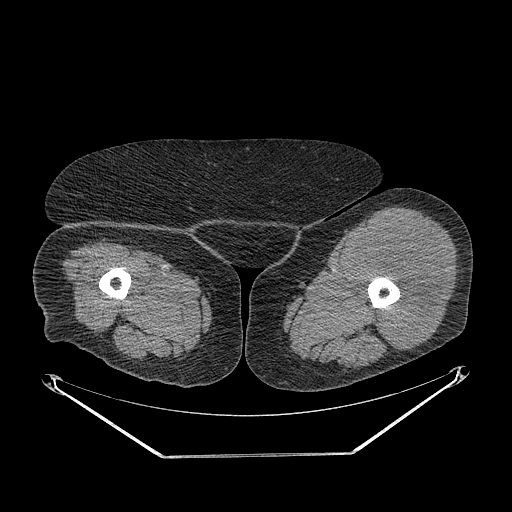
CT of an extremity soft-tissue mass (from a PET/CT study), one axial slice; position 238 of 267 along the scan axis; 140 kVp; soft-tissue window (W 400 / L 40 HU); 512 × 512 image matrix, field of view 500 × 500 mm. Female patient. From the clinical record (not read from this slice): histological type: undifferentiated – high grade; grade: high; site of the primary tumour: left thigh.
Outlined on this slice (expert contour drawn on MRI and transferred to this co-registered scan by the dataset authors):
- gross tumour volume including surrounding oedema: bounding box [x1, y1, x2, y2] px = [352, 226, 444, 350]
- gross tumour volume (mass): [352, 226, 444, 350]